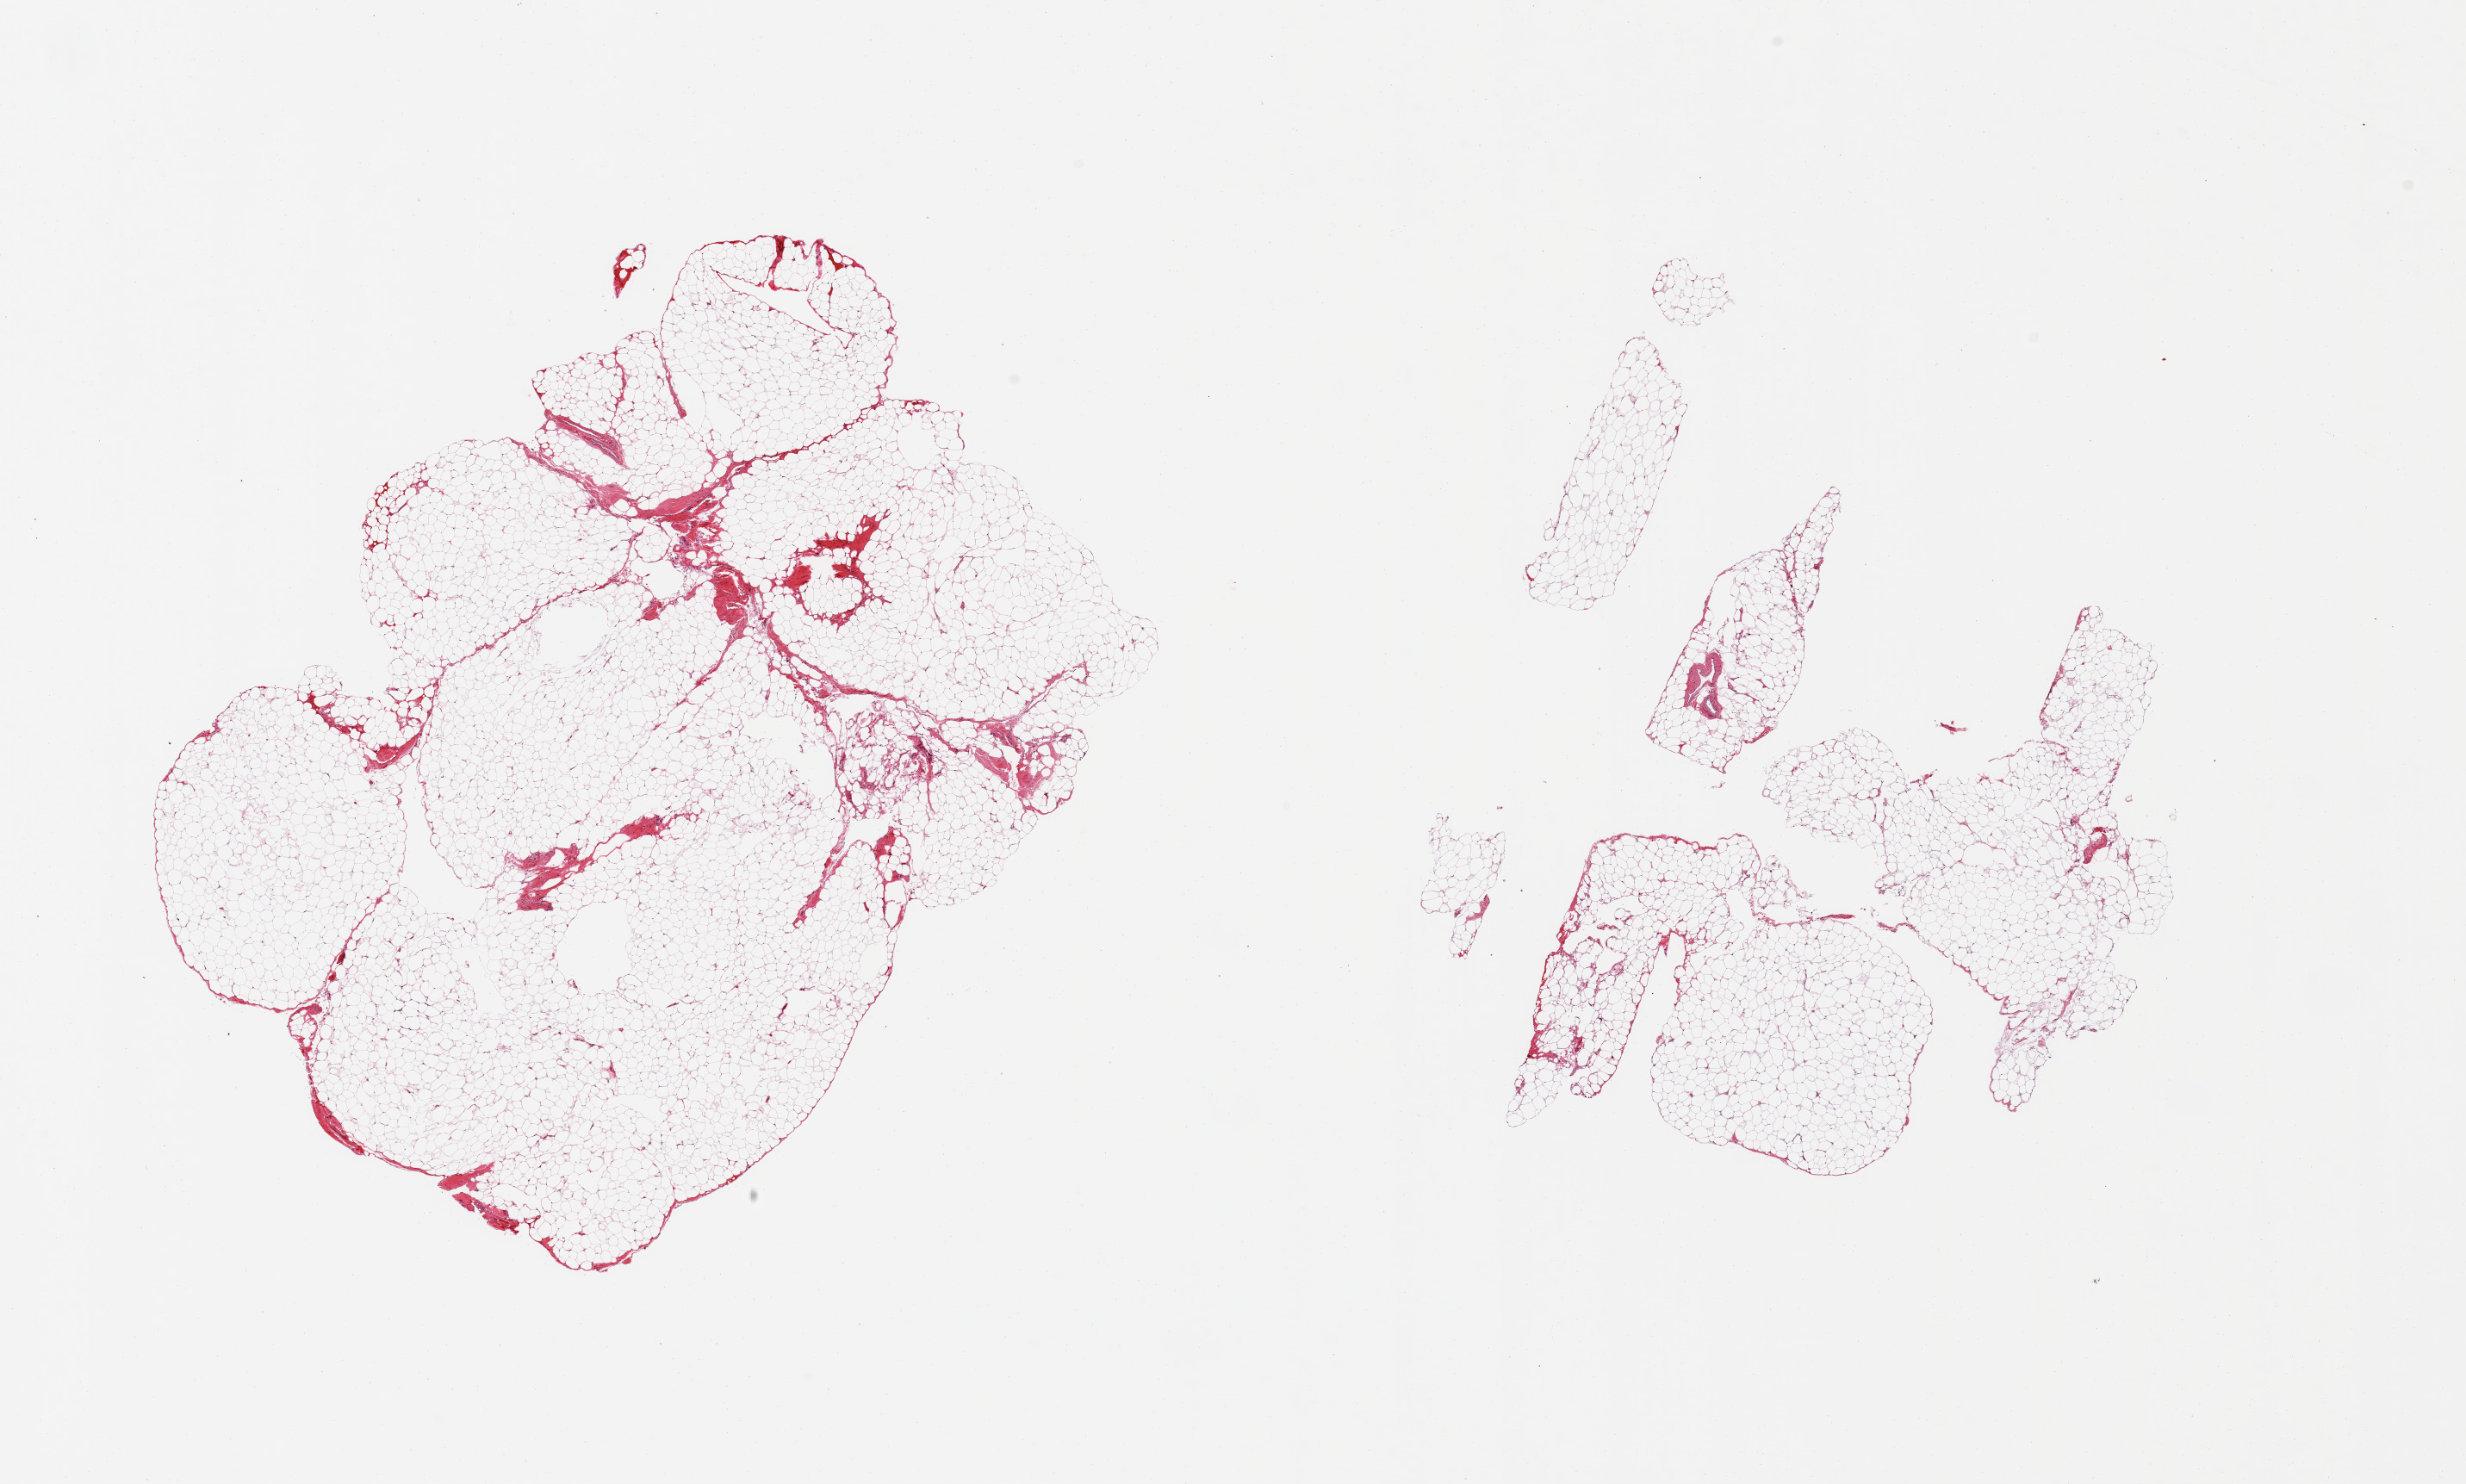
Digitized hematoxylin and eosin (H&E)-stained section, brightfield, shown as a low-resolution overview of the whole scanned area (about 22.6 x 13.6 mm, from a 20x scan); PAXgene-fixed, paraffin-embedded tissue; section of omentum (target tissue); tissue donor sample. Donor sex: male.
• pathologist's review note for this sample: 2 pieces, ~5-10% fascia